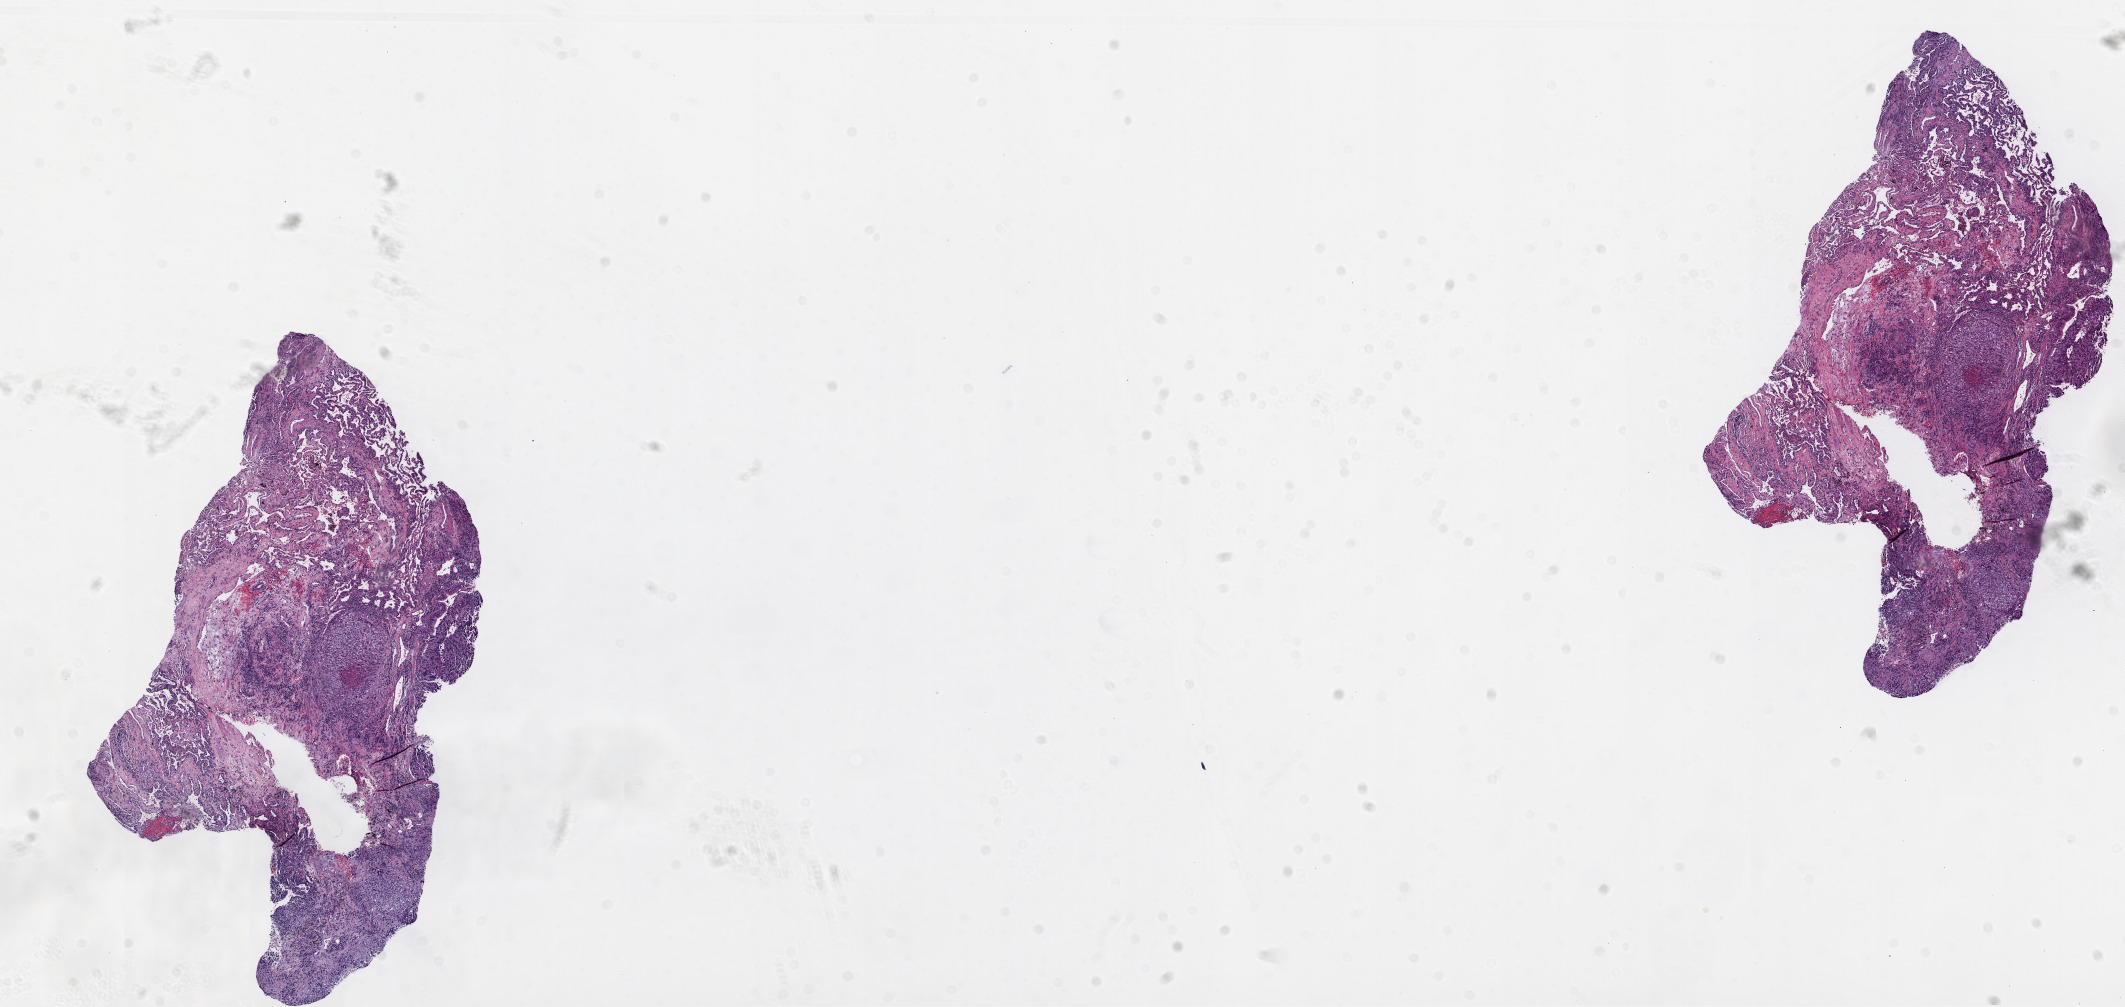
H&E-stained whole-slide image — a low-resolution overview of the entire scanned area, about 17.1 x 8.1 mm (slide scanned at 20x); frozen section; primary tumour sample from the lung. Patient: female, age at initial diagnosis 59 years. Composition of this section per pathologist review: tumour cells 60%, tumour nuclei 80%, normal cells 25%, stromal cells 10%, necrosis 5%.
AJCC pathologic stage: IA (6th edition). Histologic diagnosis: Squamous cell carcinoma, NOS (upper lobe, lung).